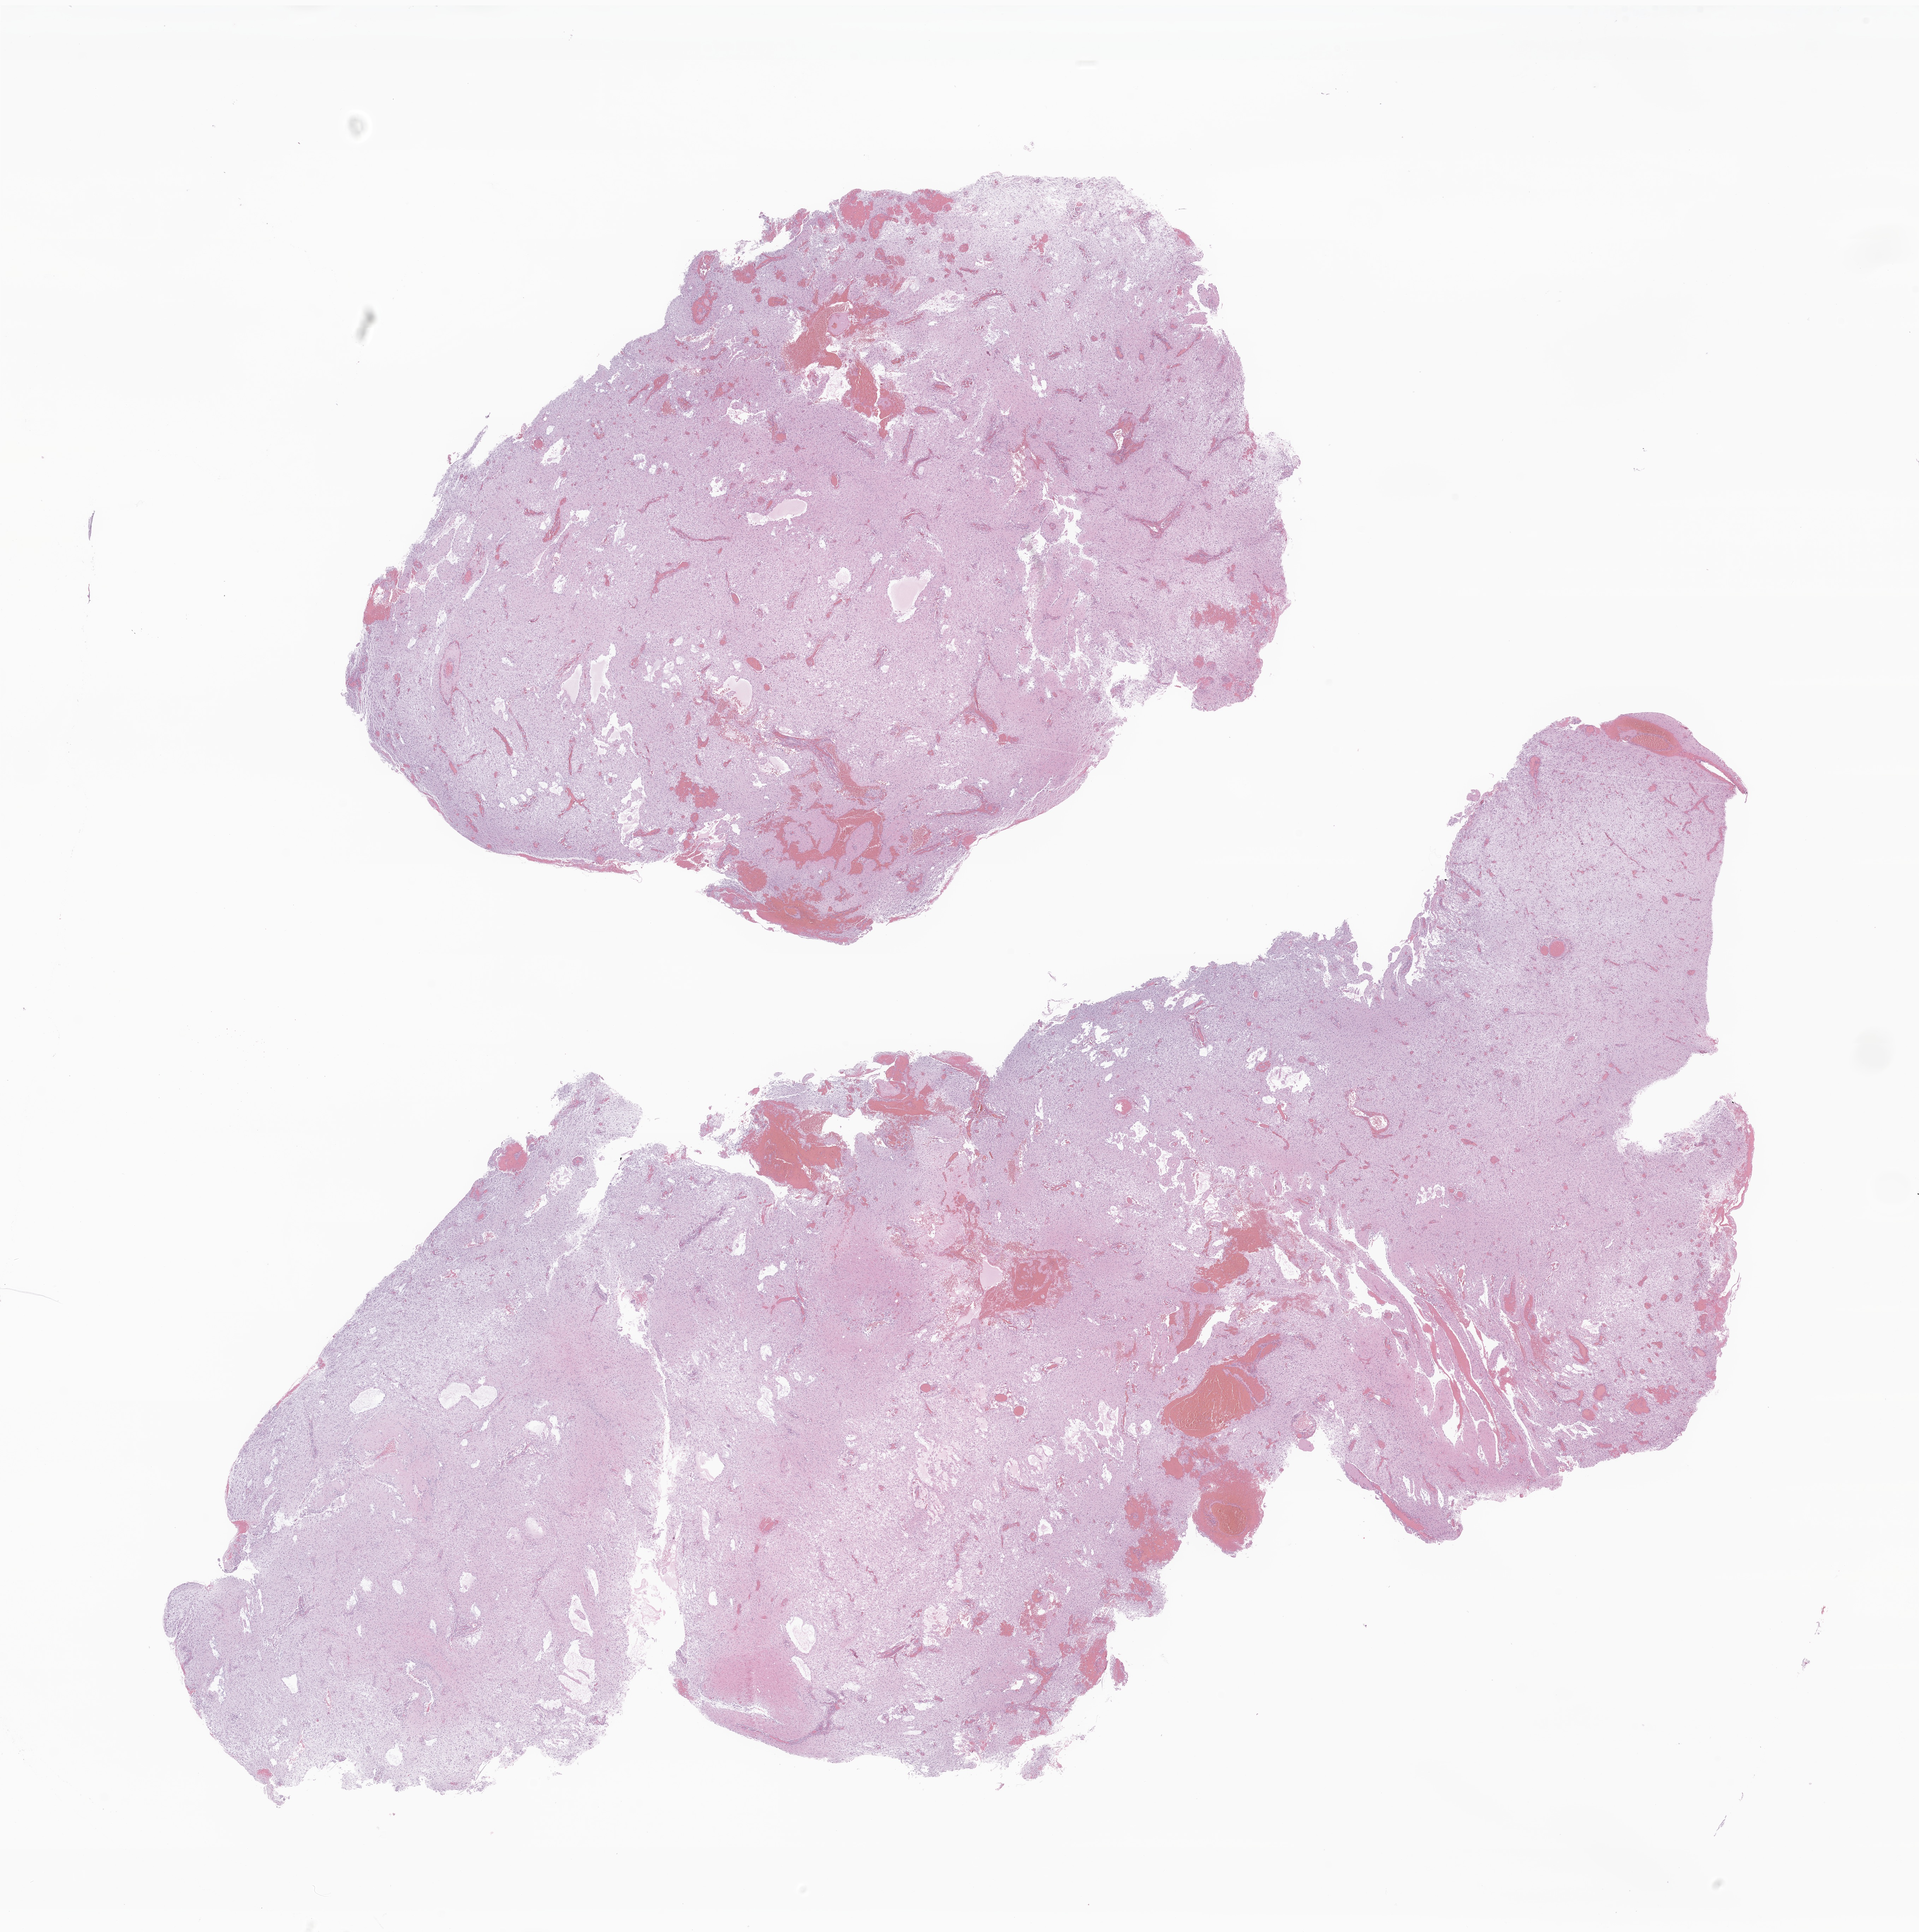
Digitized H&E-stained section of tumor tissue from the brain, whole scanned area (about 22.9 x 23.1 mm) shown as a low-resolution overview. Formalin-fixed paraffin-embedded section. Patient: female, age 89 months (7 years 5 months).
Diagnosis: Pilocytic astrocytoma.